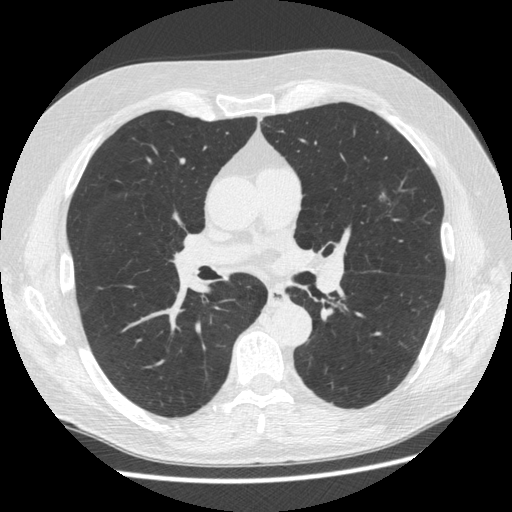
Low-dose screening chest CT, one axial slice; position 306 of 545 along the scan axis; 120 kVp; lung window (W 1500 / L -600 HU); 1.25 mm slice thickness; 512 × 512 image matrix.
Annotated regions visible in this slice (expert manual segmentation):
- lesion 1 (nodule, upper lobe of left lung): bounding box (x1, y1, x2, y2) in pixels: (379, 192, 386, 201)